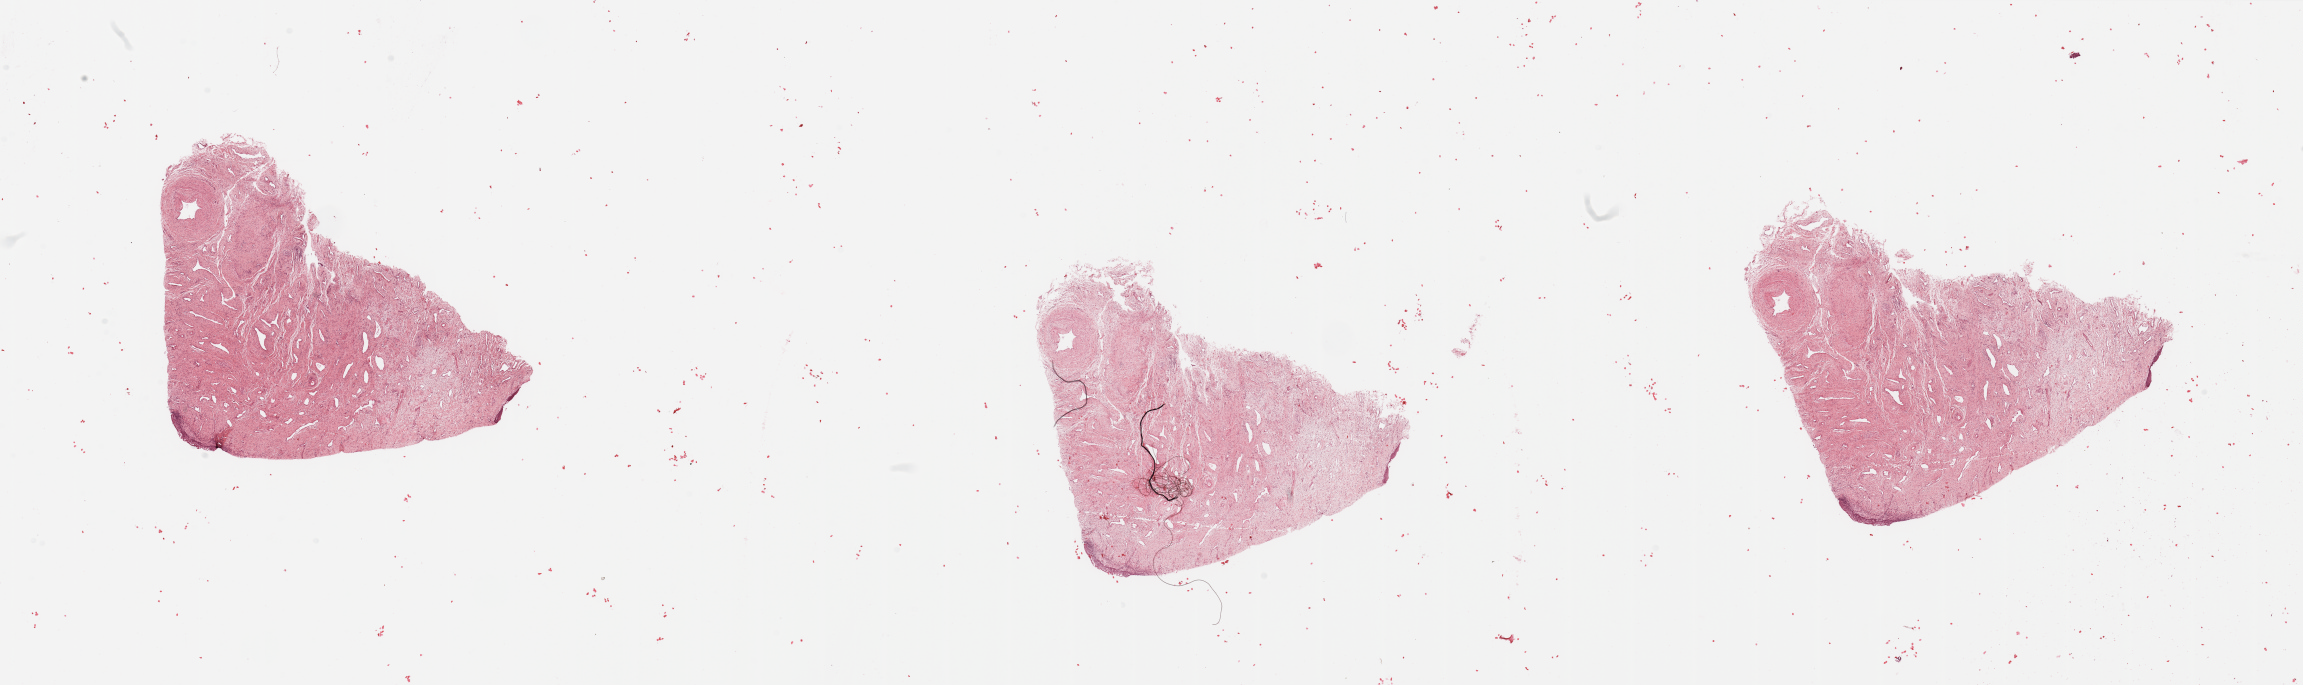
Digitized H&E tissue section (whole slide), whole scanned area (about 36.4 x 10.8 mm, slide scanned at 20x) shown as a low-resolution overview, uterus, normal (non-tumour) tissue. 59-year-old female patient.
This section: normal (non-tumour) tissue from the same patient. Patient diagnosis: Endometrioid adenocarcinoma, NOS.